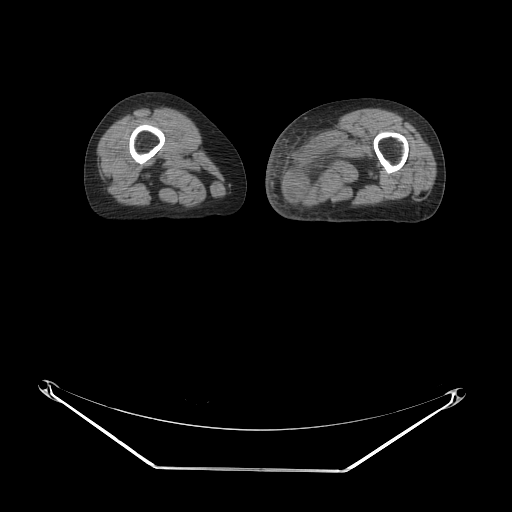
CT of an extremity soft-tissue mass (from a PET/CT study), one axial slice. Reconstruction kernel STANDARD. 140 kVp. Soft-tissue window (W 400 / L 40 HU). 3.75 mm slice thickness. 512 × 512 image matrix. Female patient. Case-level facts recorded for this patient, not image findings: histological type: pleomorphic leiomyosarcoma; grade: high; site of the primary tumour: left thigh.
Annotated regions visible in this slice (expert contour drawn on MRI and transferred to this co-registered scan by the dataset authors):
- gross tumour volume including surrounding oedema: bounding box [x1, y1, x2, y2] px = [288, 130, 373, 200]
- gross tumour volume (mass): [288, 162, 321, 200]